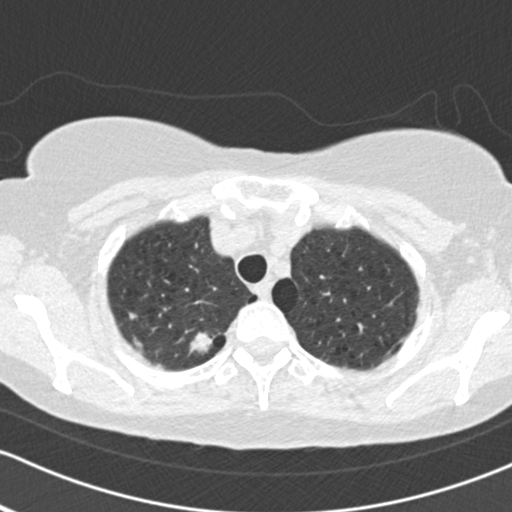
Low-dose screening chest CT, one axial slice; slice 141 of 161 in the series (ordered by position); reconstruction kernel B30f; lung window (W 1500 / L -600 HU); 2 mm slice thickness; 512 × 512 image matrix.
Structures marked on this image (expert manual segmentation):
- lesion 1 (tumor, upper lobe of right lung): box from (x=189, y=332) to (x=214, y=354) px